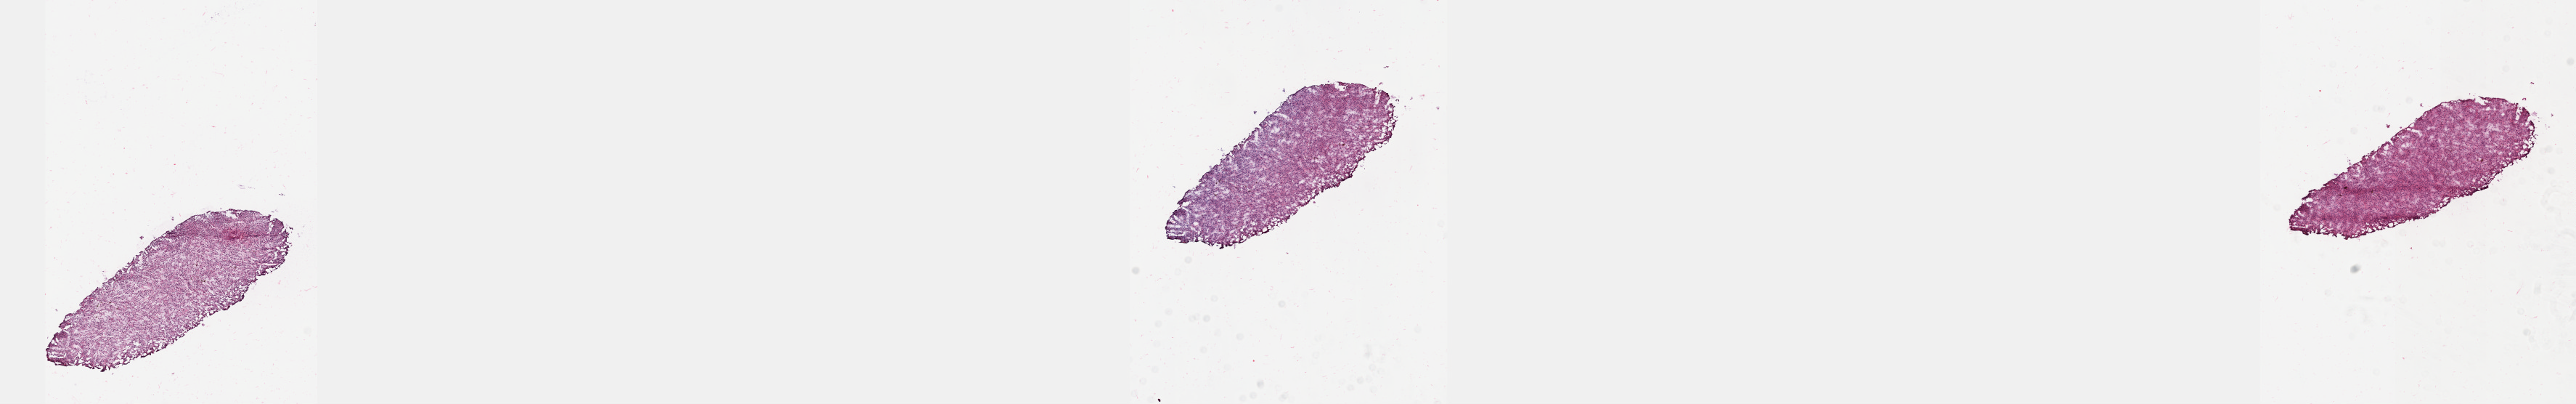
H&E whole-slide image — a low-resolution overview of the entire scanned area, about 28.7 x 4.5 mm (from a 40x scan). Frozen section from the top of the tissue portion. Primary tumour sample from the uvea. Patient: male, age at initial diagnosis 54 years. Slide review estimates, as recorded: tumour cells 100%, tumour nuclei 80%, normal cells 0%, stromal cells 0%, necrosis 0%. Inflammatory infiltration, as recorded: lymphocyte infiltration 1%, monocyte infiltration 0%, neutrophil infiltration 0%.
TNM: T3a NX MX. AJCC pathologic stage: IIB. Pathologic diagnosis: Epithelioid cell melanoma (choroid). Laterality: right.